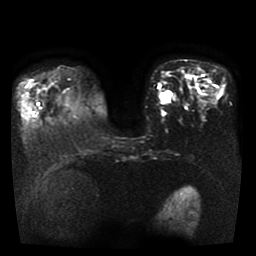
Breast MRI, one axial slice. Slice 13 of 41 in the series (ordered by position). Diffusion-weighted series; image 2 of 4 stored at this slice position (different b-values; order by instance number). 1.5 T. 256 × 256 image matrix. Female patient.
Outlined on this slice (manually delineated by an expert):
- tumour on diffusion-weighted imaging: bounding box <159,91,172,104> (left, top, right, bottom; pixels)